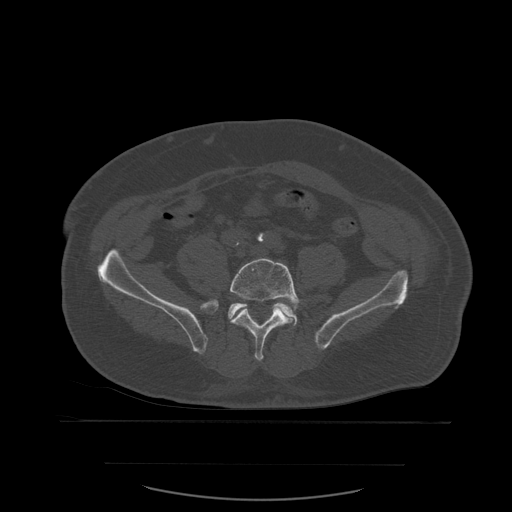
CT including the spine, one axial slice. Slice 135 of 590 in the series (ordered by position). Bone window (W 1800 / L 400 HU). 1.25 mm slice thickness. 512 × 512 image matrix, field of view 479 × 479 mm. Patient age 71 years. From the clinical record (not read from this slice): primary cancer: lung; vertebrae with lytic lesions (as recorded): T1, T2, L5, S1.
Outlined on this slice (semi-automatic segmentation, software-assisted and operator-edited):
- L5 vertebra: box from (x=230, y=258) to (x=301, y=361) px